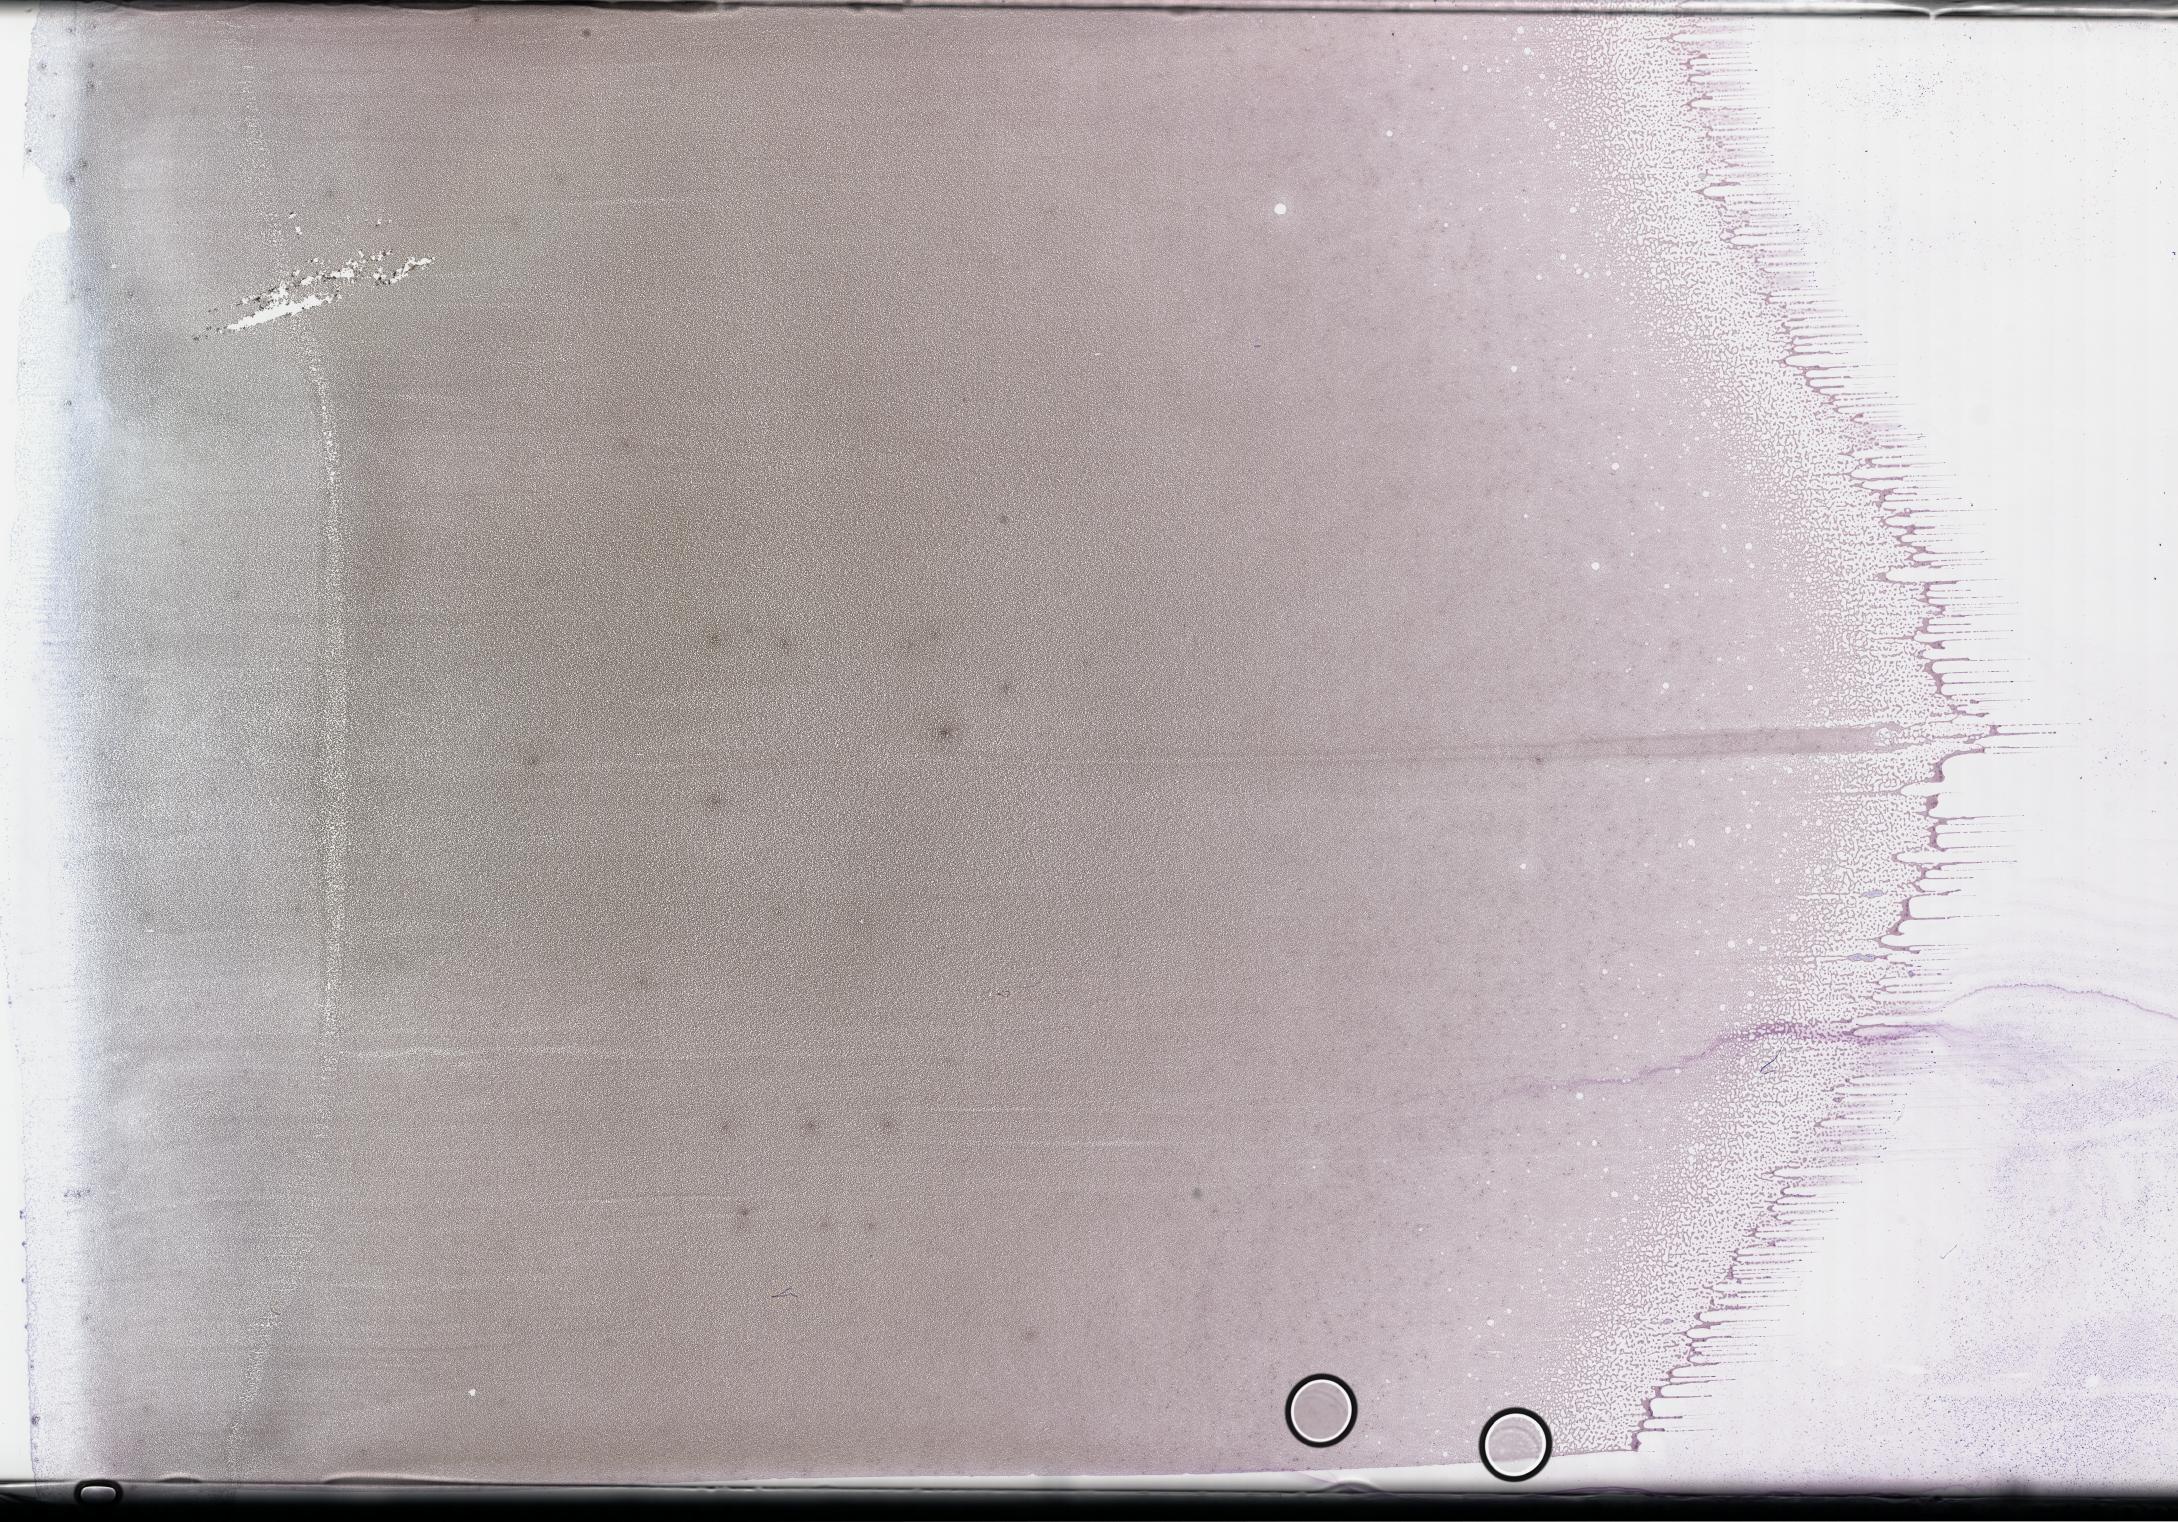
Wright–Giemsa-stained whole blood smear, whole-slide image — a low-resolution overview of the entire scanned area, about 35.2 x 24.6 mm. Collected at baseline (before treatment). Male patient.
Patient diagnosis: Plasma Cell Myeloma.